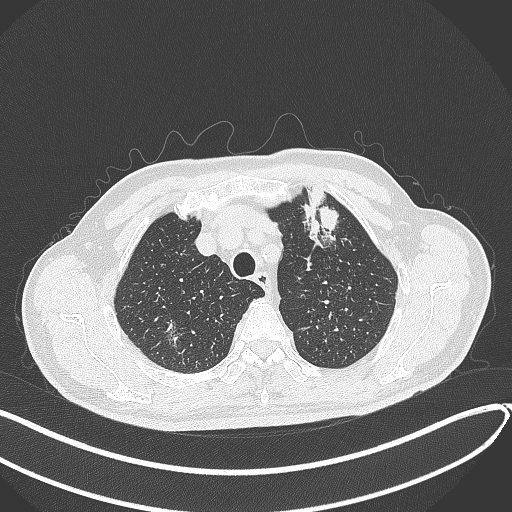
Chest CT, one axial slice. Position 347 of 459 along the scan axis. Reconstruction kernel B70f. Lung window (W 1500 / L -600 HU). 512 × 512 image matrix, field of view 400 × 400 mm. Male patient, age 74 years. From the clinical record (not read from this slice): clinical TNM (as recorded): T2b N0 M1c.
Annotated regions visible in this slice (rectangle marked by the reading radiologist):
- lung tumour (recorded histology: adenocarcinoma): box from (x=298, y=182) to (x=348, y=248) px